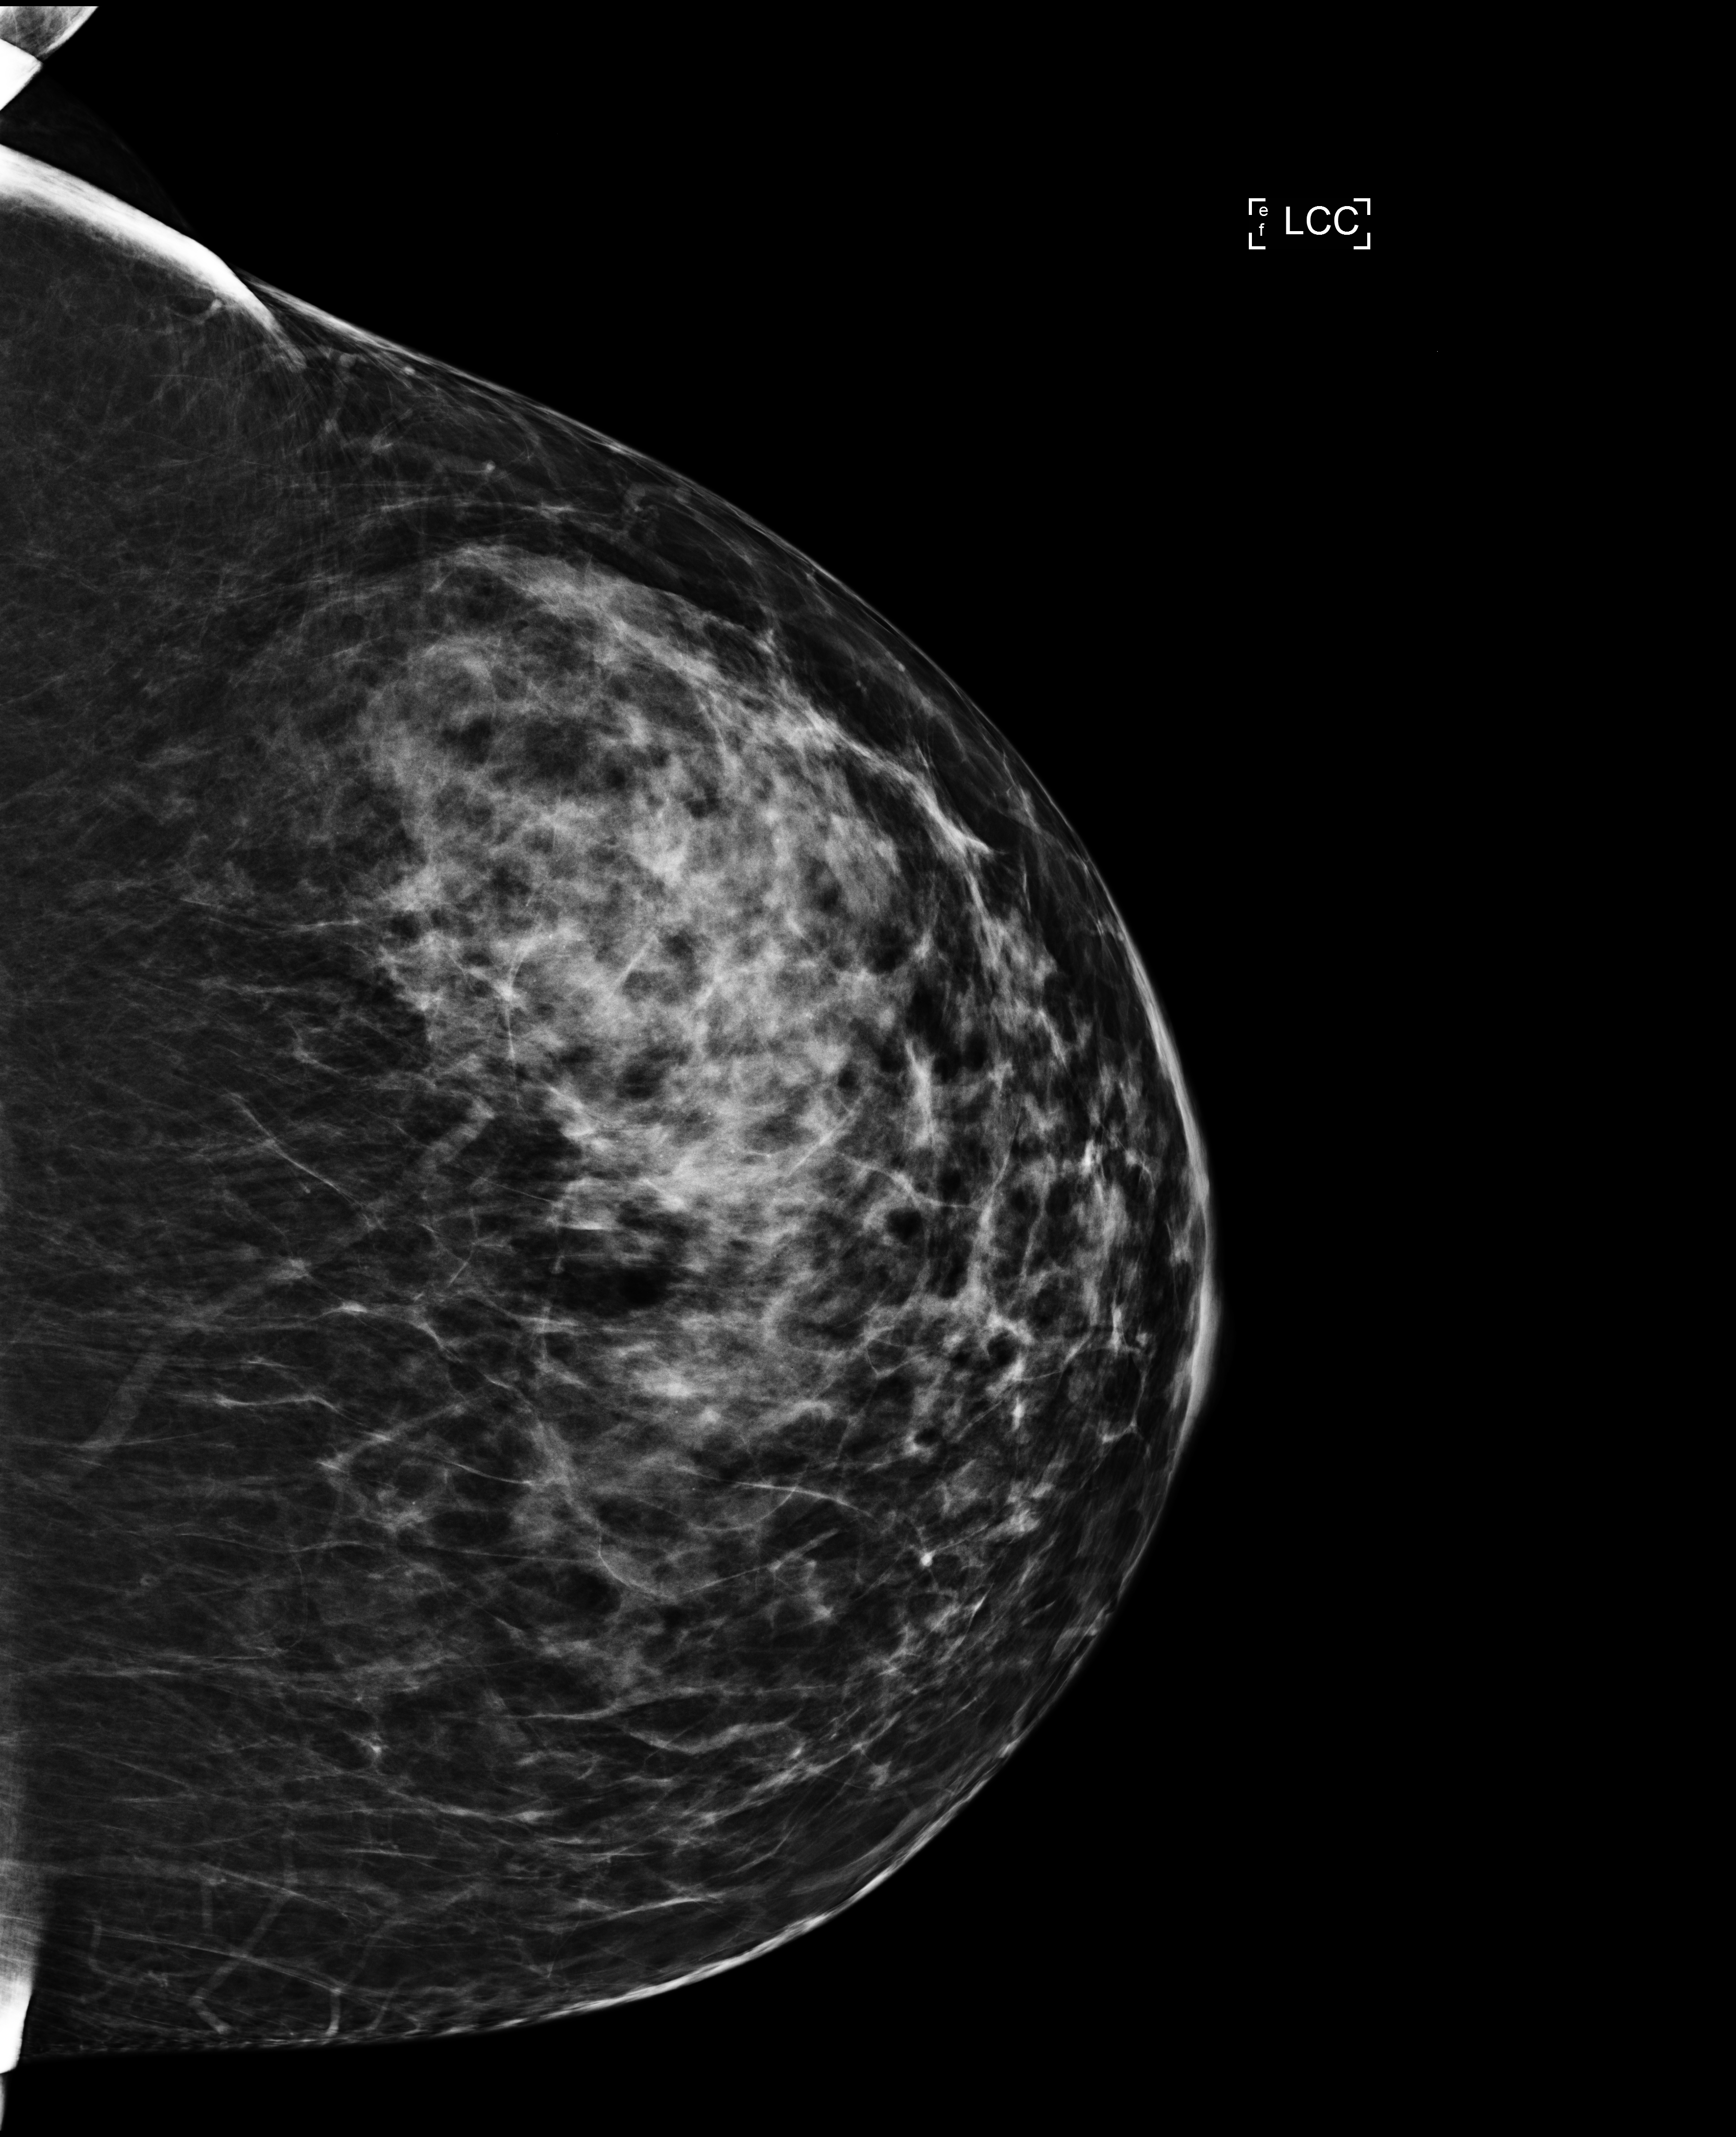
Full-field digital mammogram (FFDM); left breast; CC view; annual screening mammography examination. Female patient, age 49 years.
BI-RADS breast density category at the screening exam (both breasts, scale 1–4): 3. Final BI-RADS category for the screening round (tomosynthesis exam, both breasts): category 1. Recall: no recall after this screen.